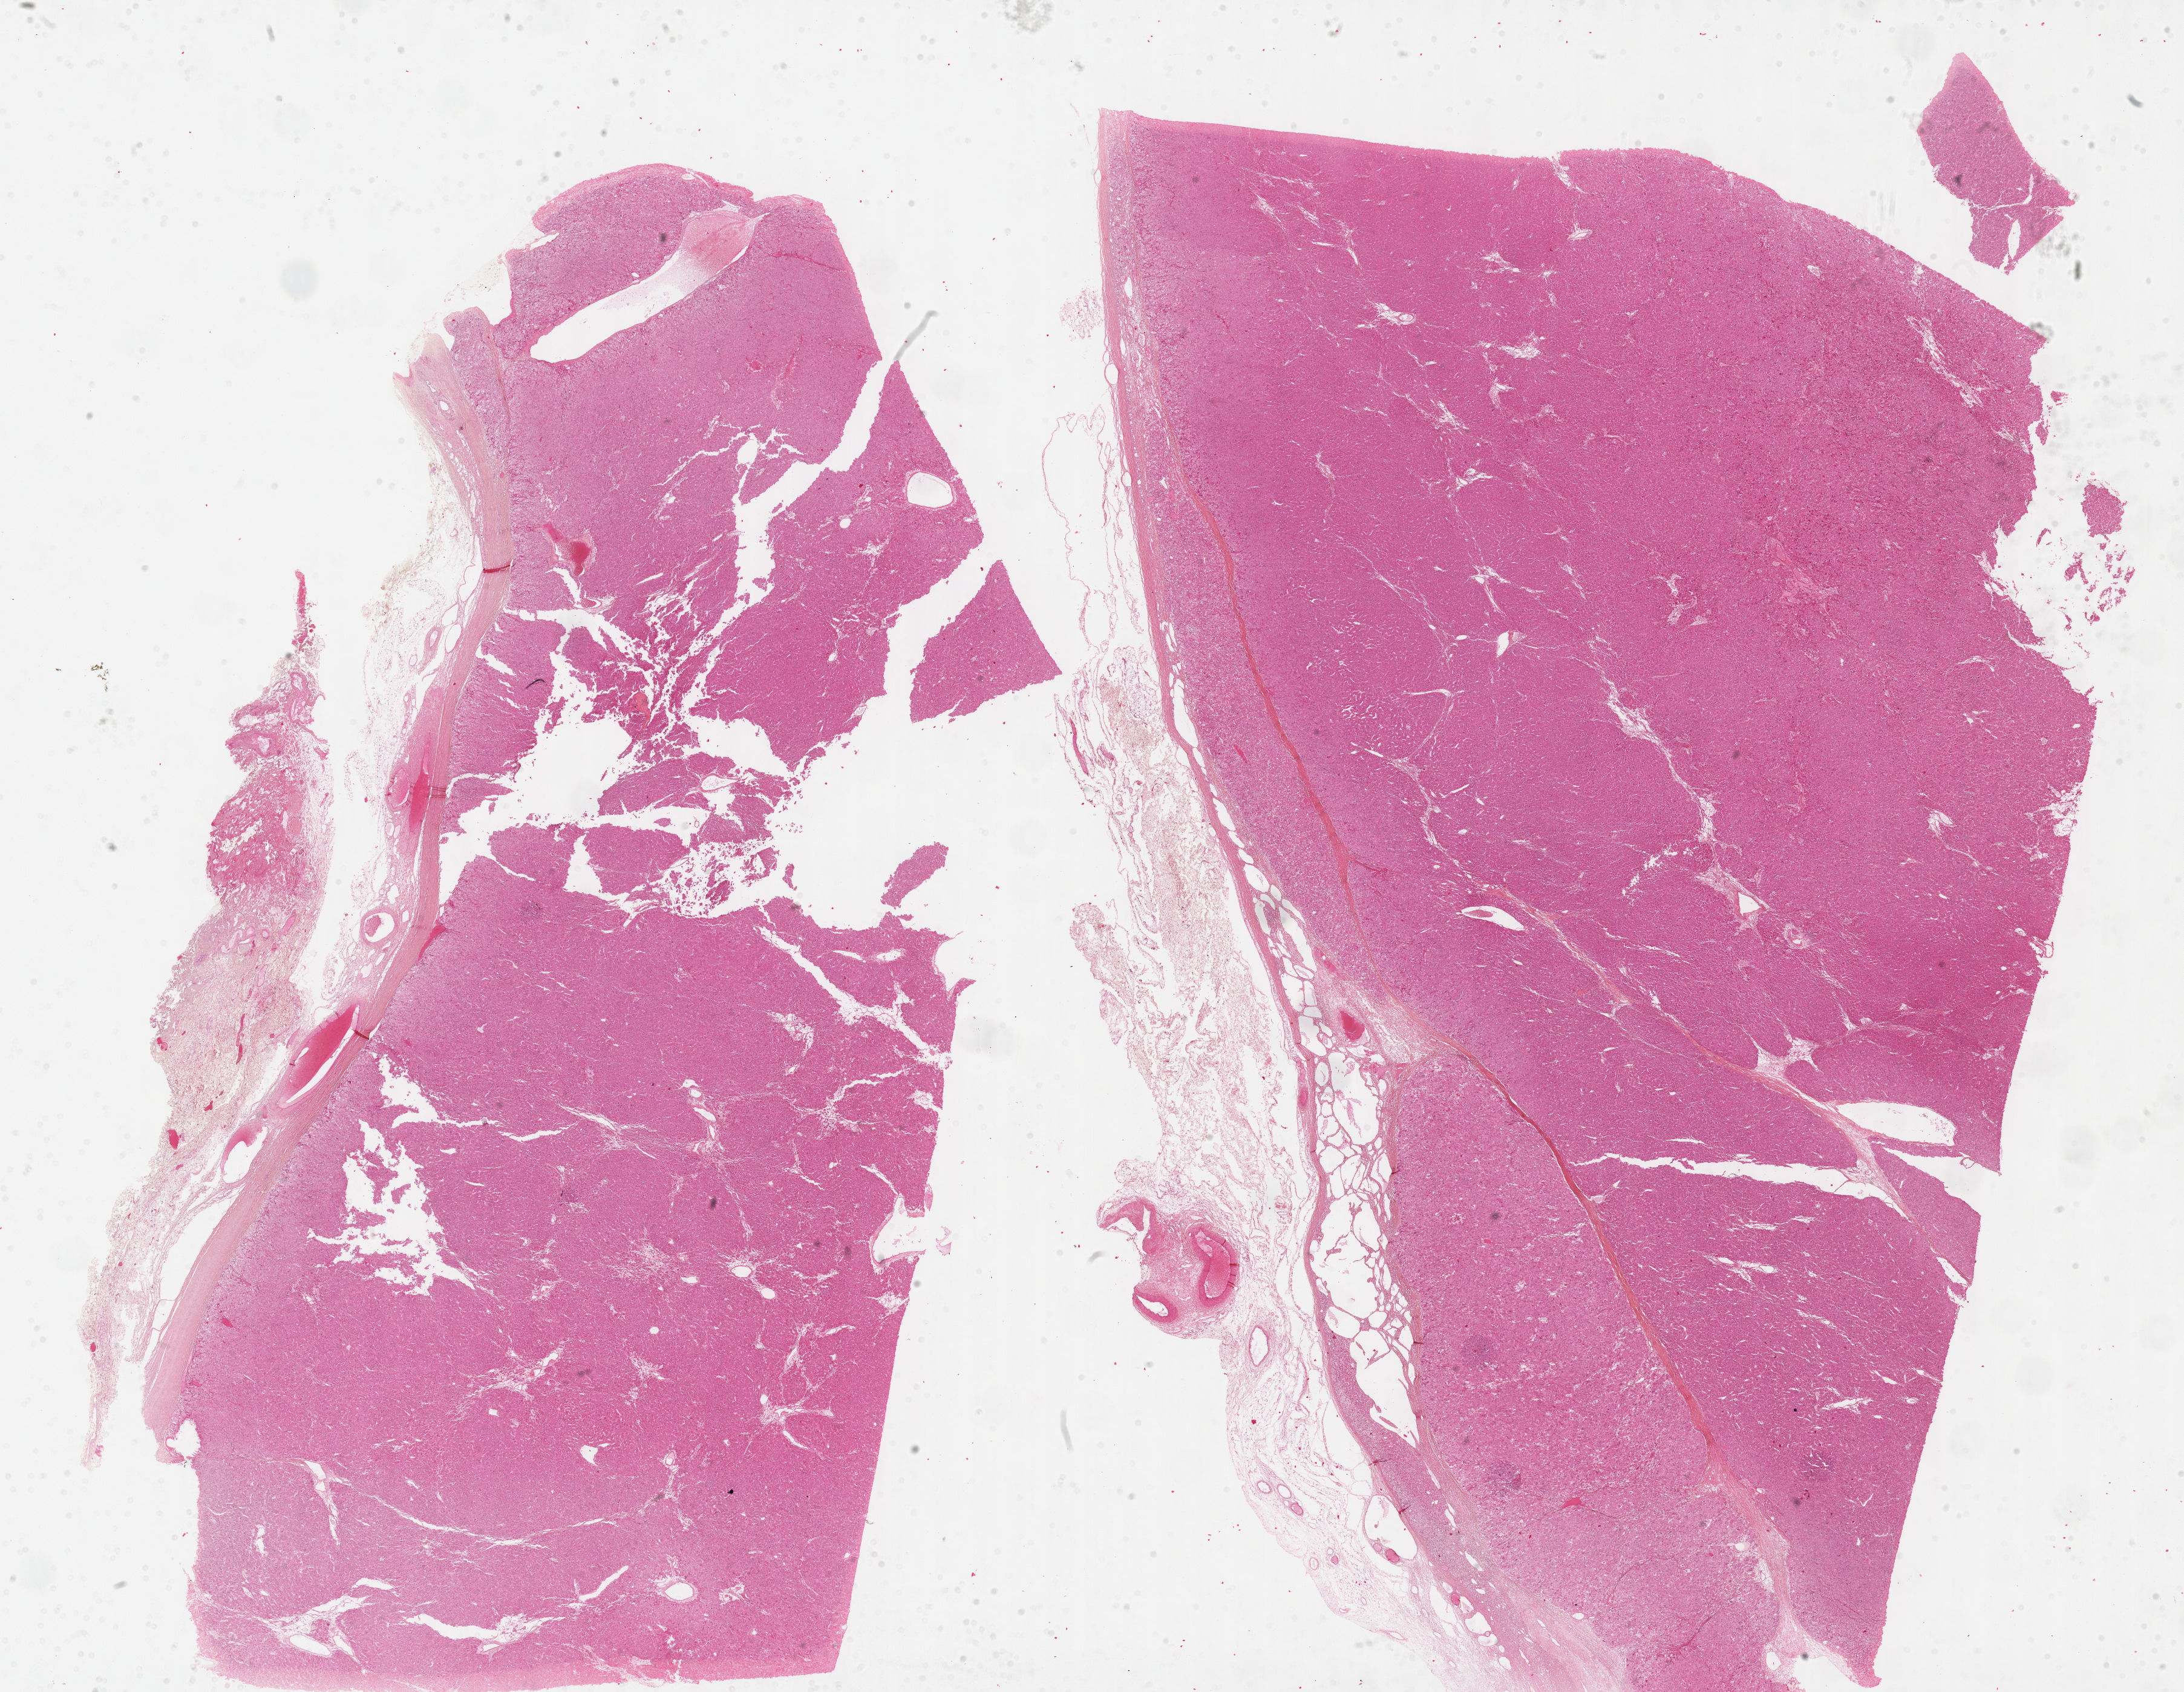
Hematoxylin and eosin (H&E) stained whole-slide image, low-resolution overview of the scanned area, about 29.2 x 22.6 mm (acquisition: 40x scan), formalin-fixed paraffin-embedded (FFPE) diagnostic section, sample: primary tumour, adrenal cortex. Female patient; age at initial diagnosis 31 years.
Laterality: right. Lymph nodes positive (case pathology): 0 of 10 examined. Histologic diagnosis: Adrenal cortical carcinoma.